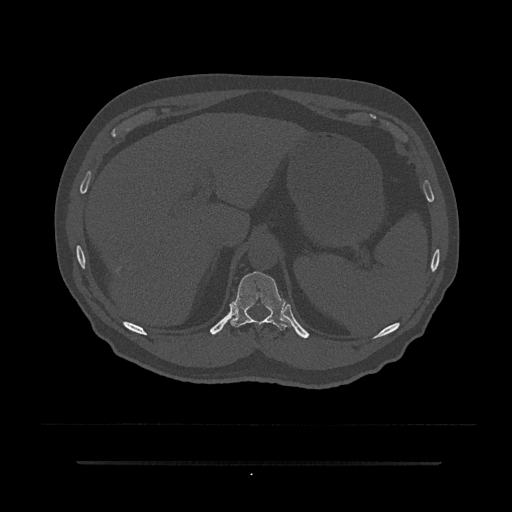
CT including the spine, one axial slice; position 275 of 797 along the scan axis; reconstruction kernel Br40s/3; 120 kVp; bone window (W 1800 / L 400 HU); 512 × 512 image matrix, field of view 464 × 464 mm. Male patient, age 59 years. From the clinical record (not read from this slice): primary cancer: bile ducts; vertebrae with lytic lesions (as recorded): T10.
Outlined on this slice (semi-automatically segmented with operator editing):
- T11 vertebra: bounding box (x1, y1, x2, y2) in pixels: (230, 271, 292, 331)